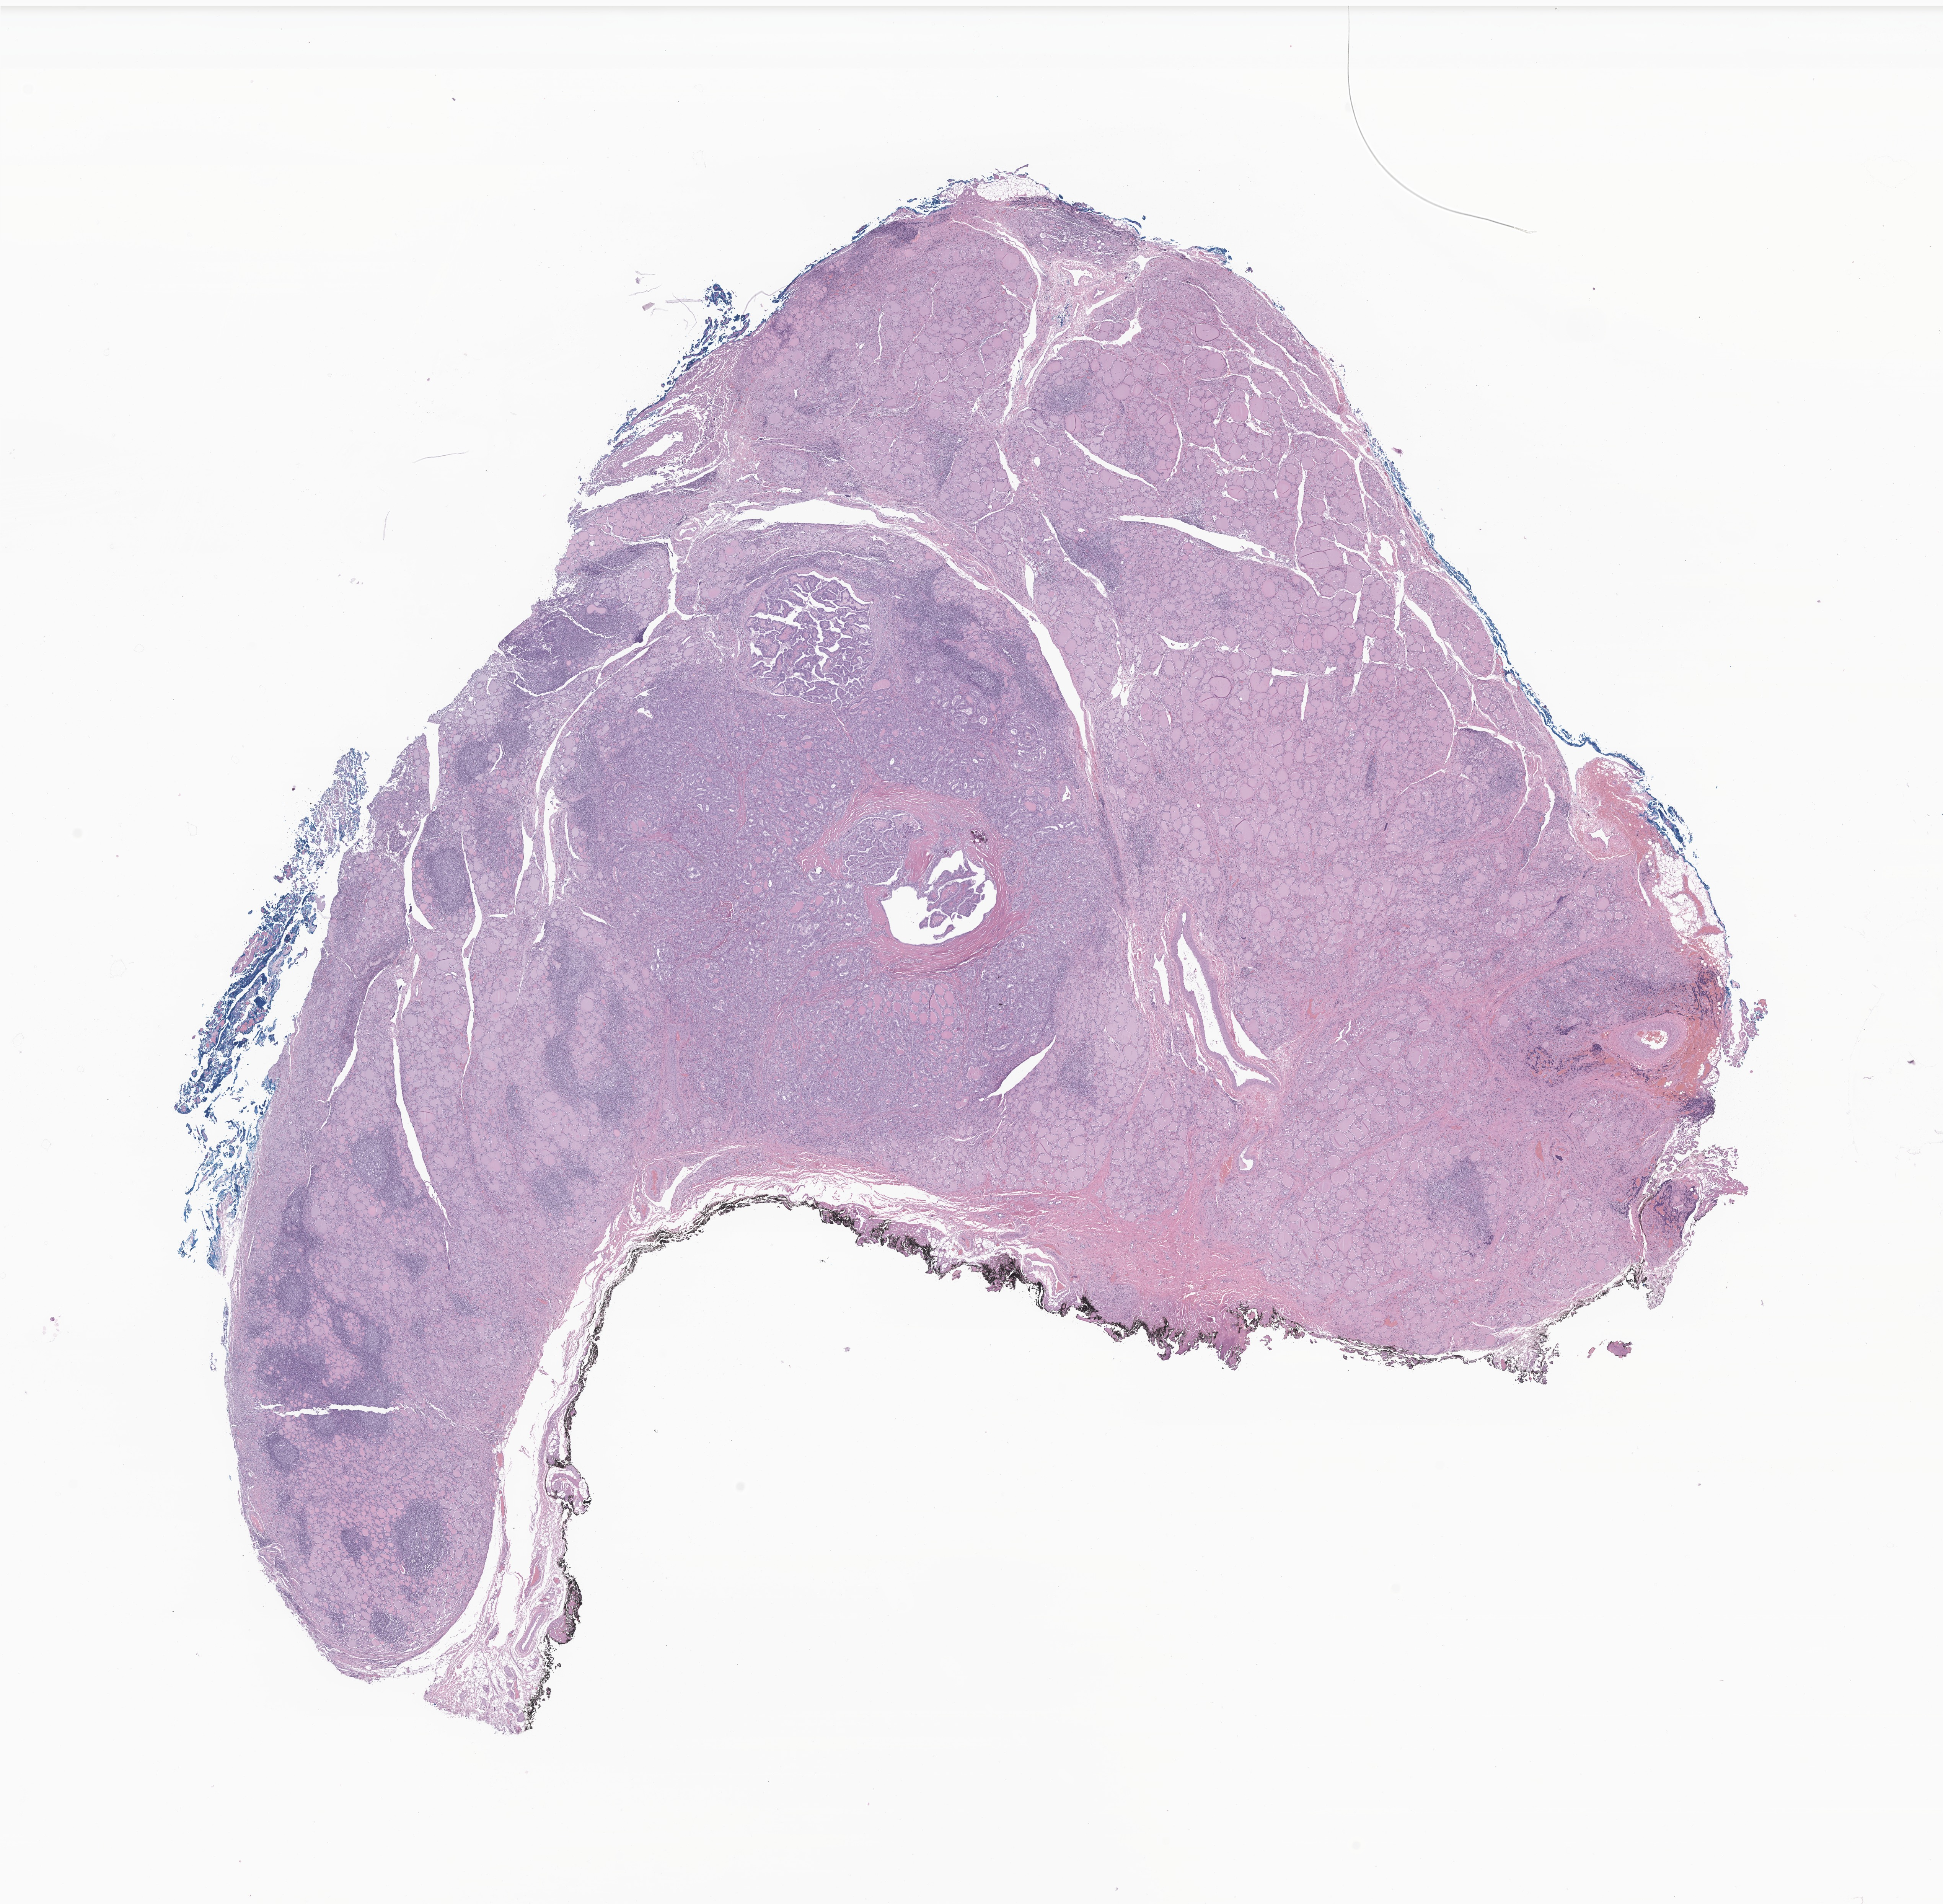
Haematoxylin and eosin whole-slide image of tumor tissue from the thyroid — low-resolution overview of the scanned area, about 21.4 x 21.0 mm; formalin-fixed, paraffin-embedded (FFPE) tissue. Patient female; age 222 months (18 years 6 months).
Diagnosis: Papillary carcinoma, NOS.